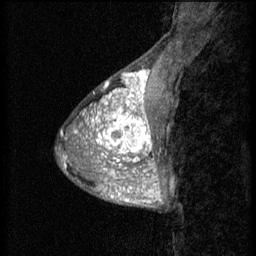
Breast MRI (dynamic contrast-enhanced), one sagittal slice. Position 18 of 60 along the scan axis. 3 images stored at this slice position (order not interpretable as contrast timing). 1.5 T. TE 4.2 ms, TR 8.2 ms. 256 × 256 image matrix, field of view 180 × 180 mm. Female patient, age 38 years.
Structures marked on this image (semi-automatically segmented with operator editing):
- analysis volume of interest (the breast-tissue region the enhancement analysis was run in; not a lesion): bounding box (x1, y1, x2, y2) in pixels: (95, 106, 157, 171)
- tumour enhancement mask (voxels above the 70 % enhancement threshold inside the analysis volume of interest): (95, 106, 156, 171)